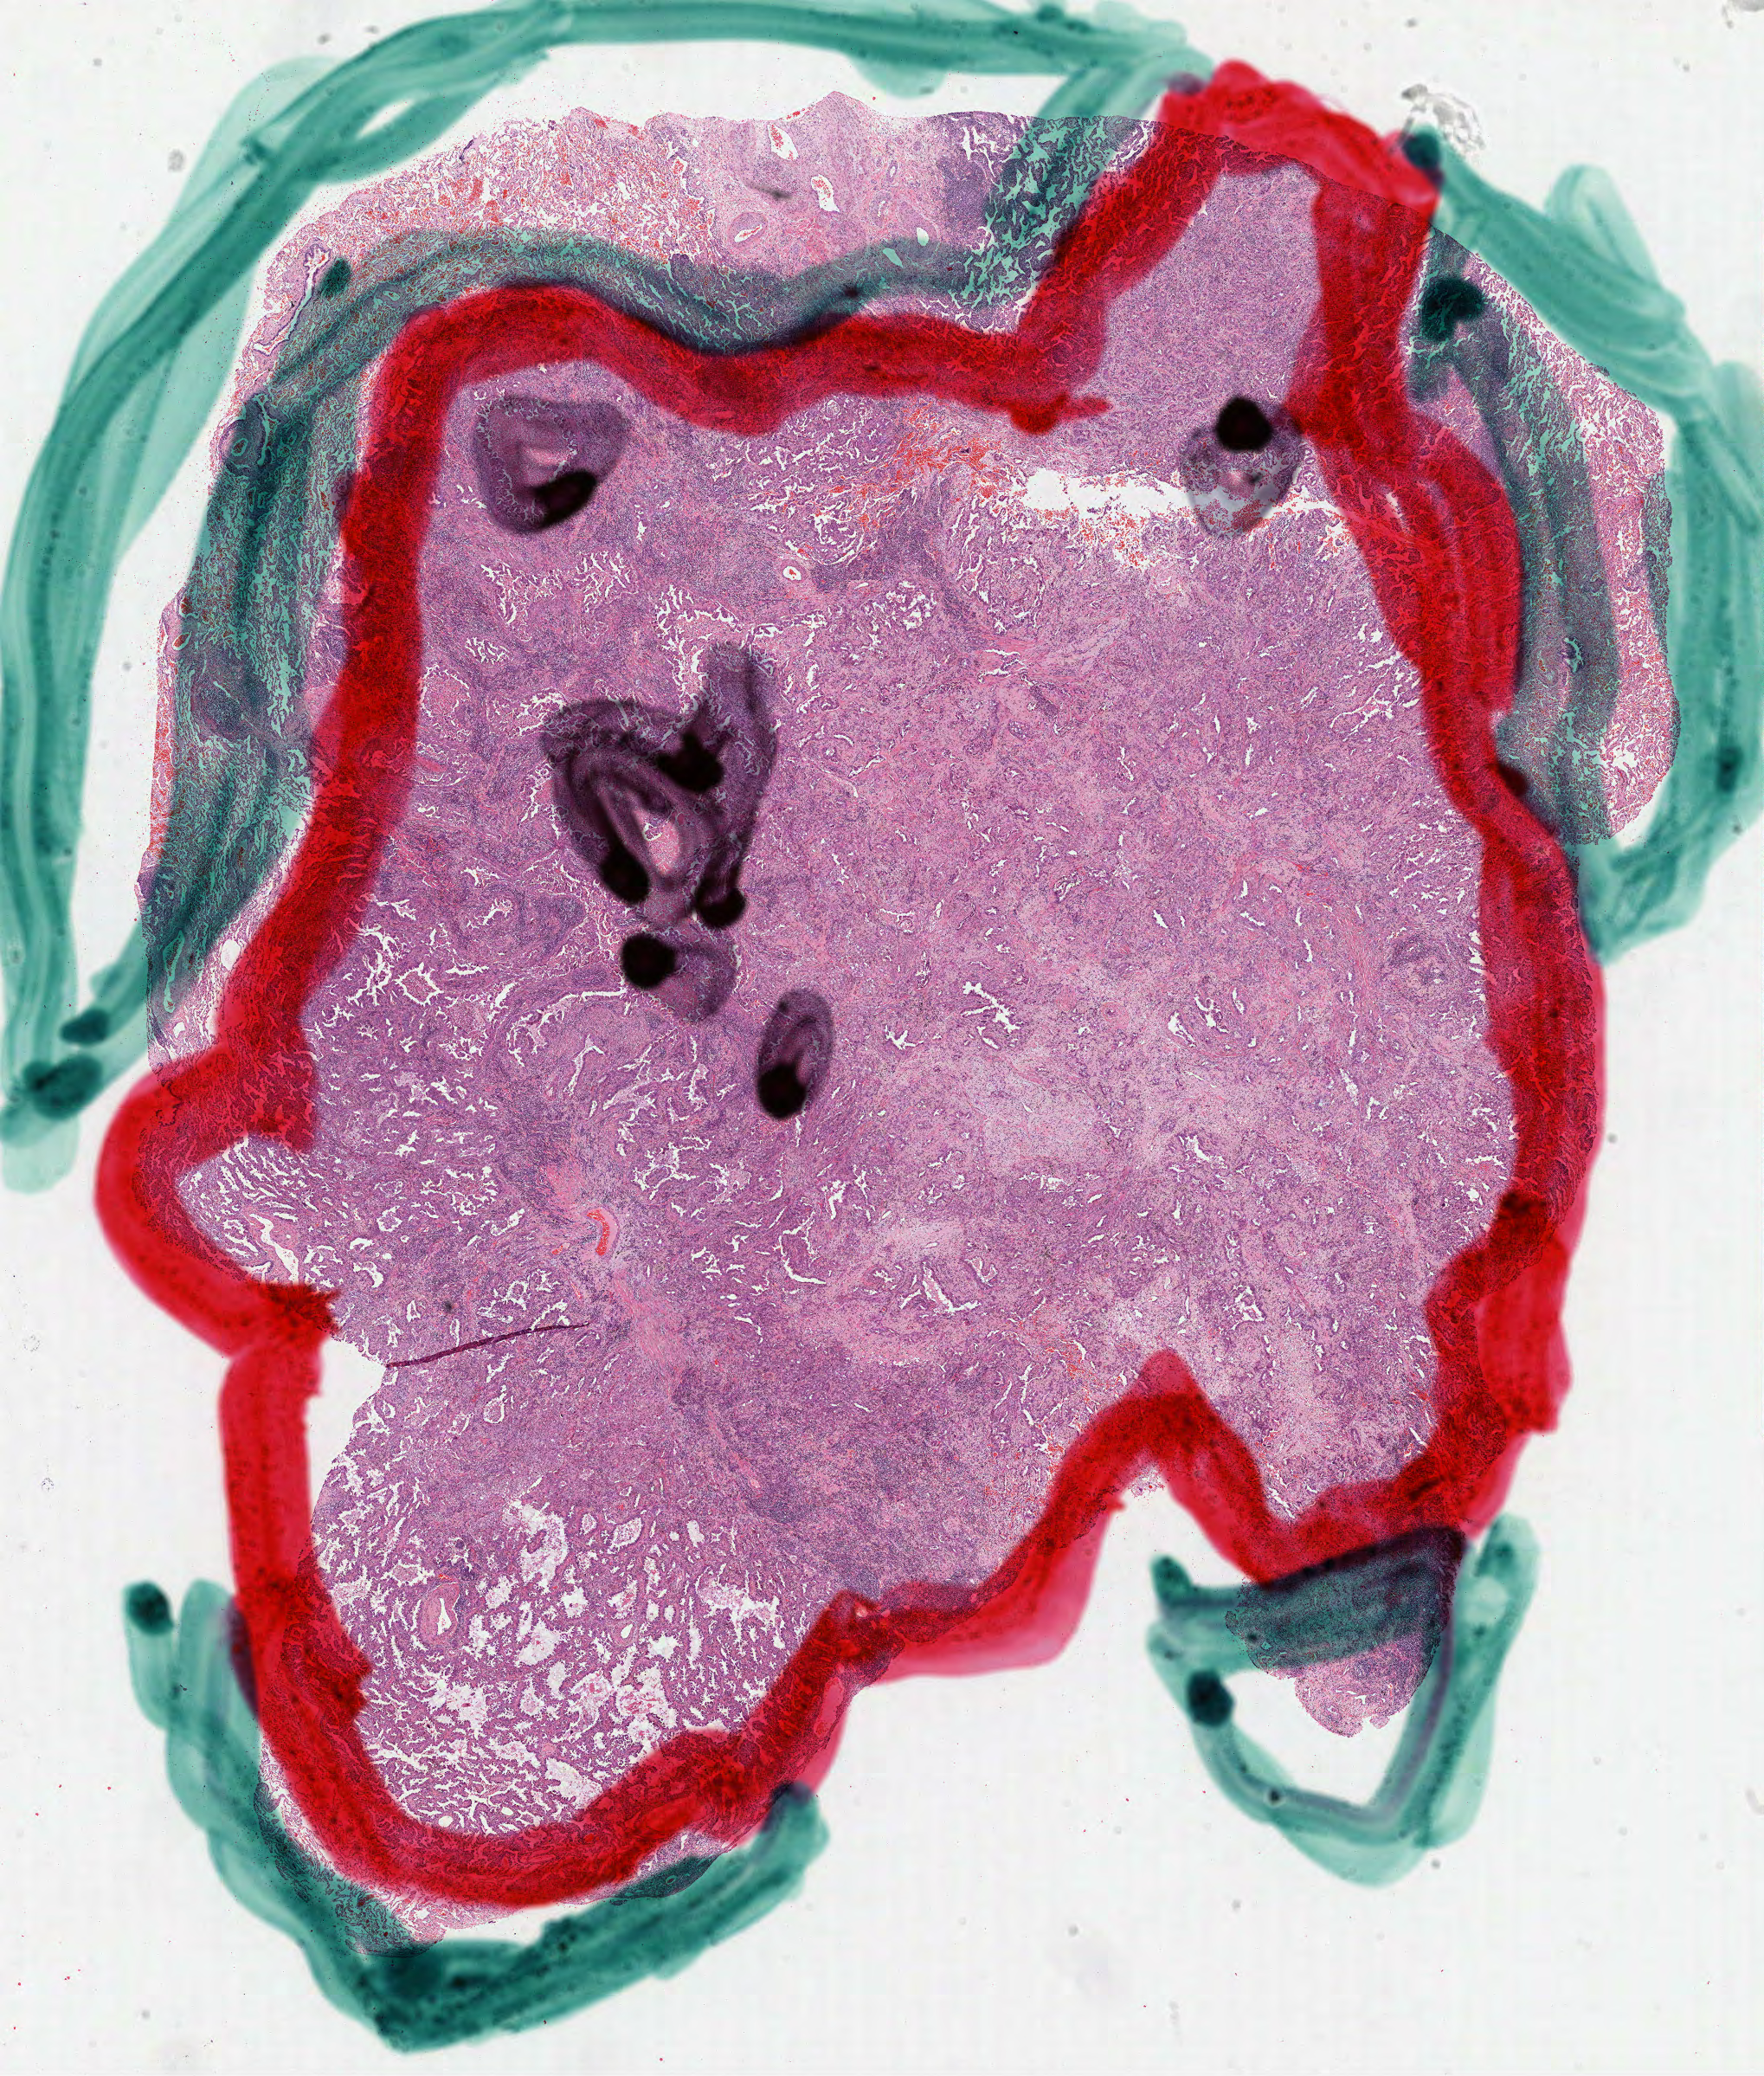
Whole-slide histology image, H&E-stained — shown as a low-resolution overview of the whole scanned area (about 16.4 x 19.3 mm, acquisition: 40x scan); FFPE section; sample: primary tumour, lung. Female, age 66 years at initial diagnosis.
- AJCC pathologic stage: IB (7th edition)
- diagnosis: Adenocarcinoma, NOS
- laterality: left